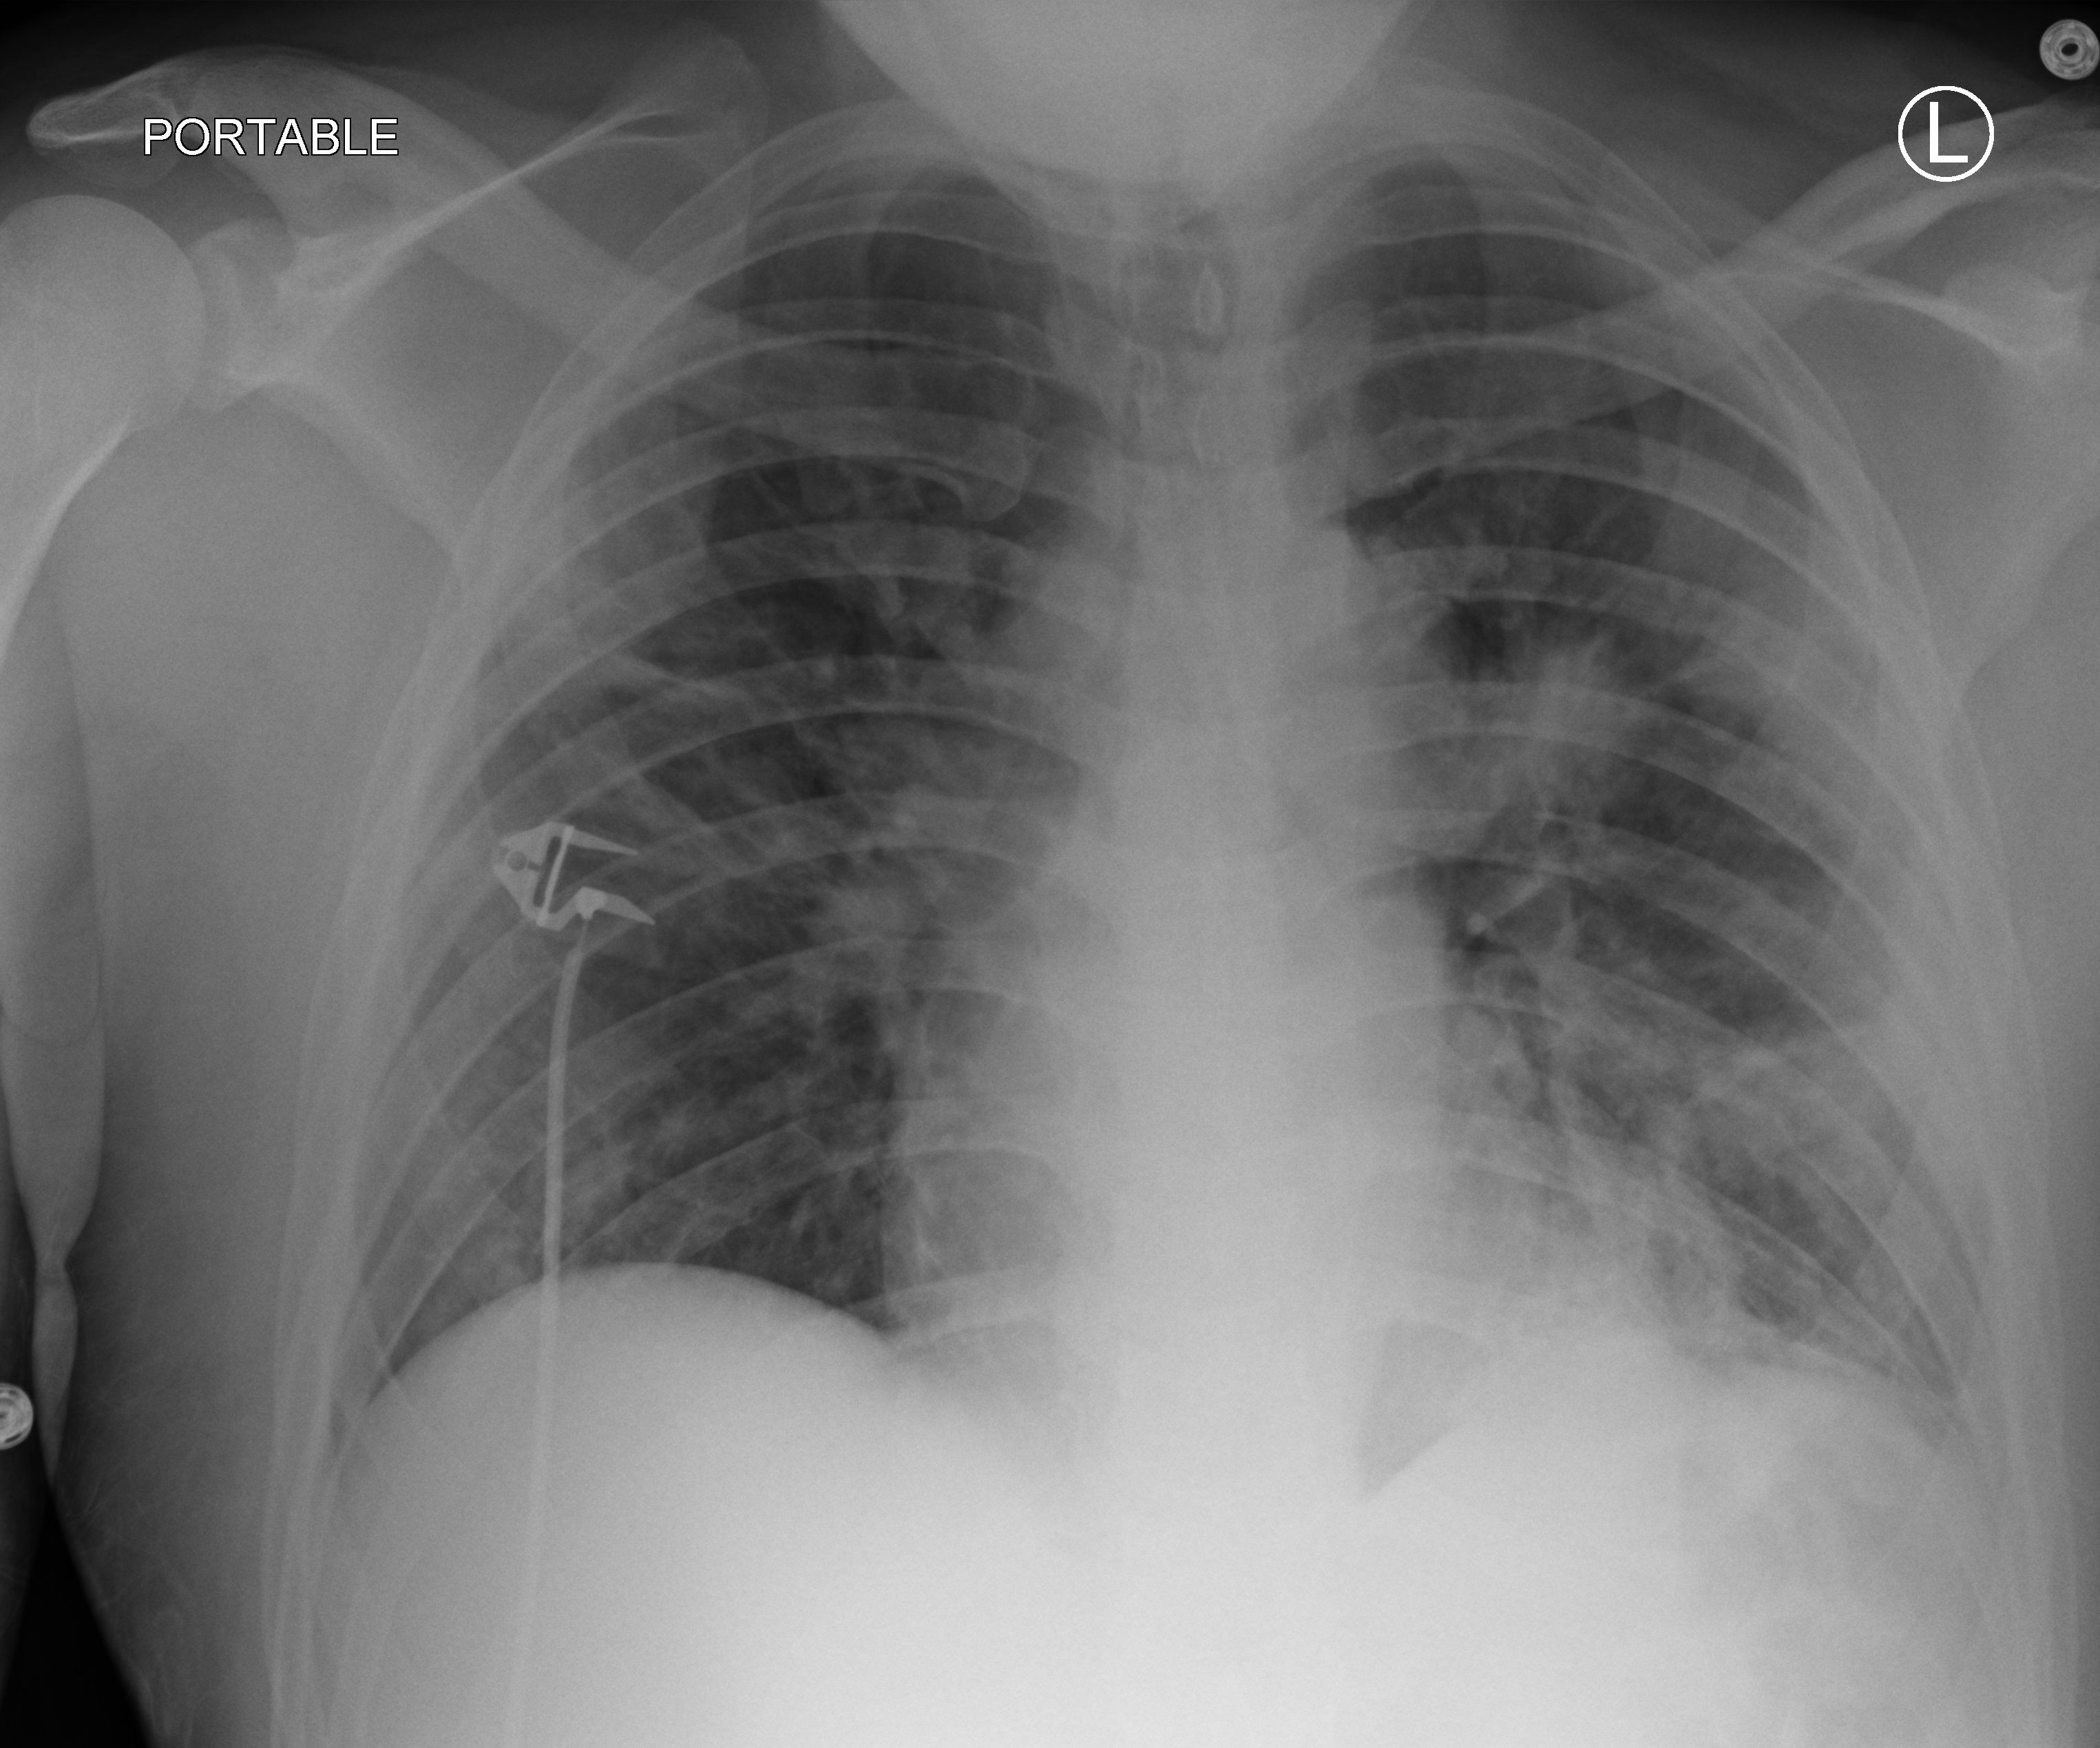
Chest X-ray (portable). Male patient hospitalised with COVID-19, age 18–59 years.
Hospital-stay facts (about this admission, not read from this image; timing relative to this image not recorded):
- mechanically ventilated during this hospital stay: no
- admitted to intensive care during this hospital stay: no